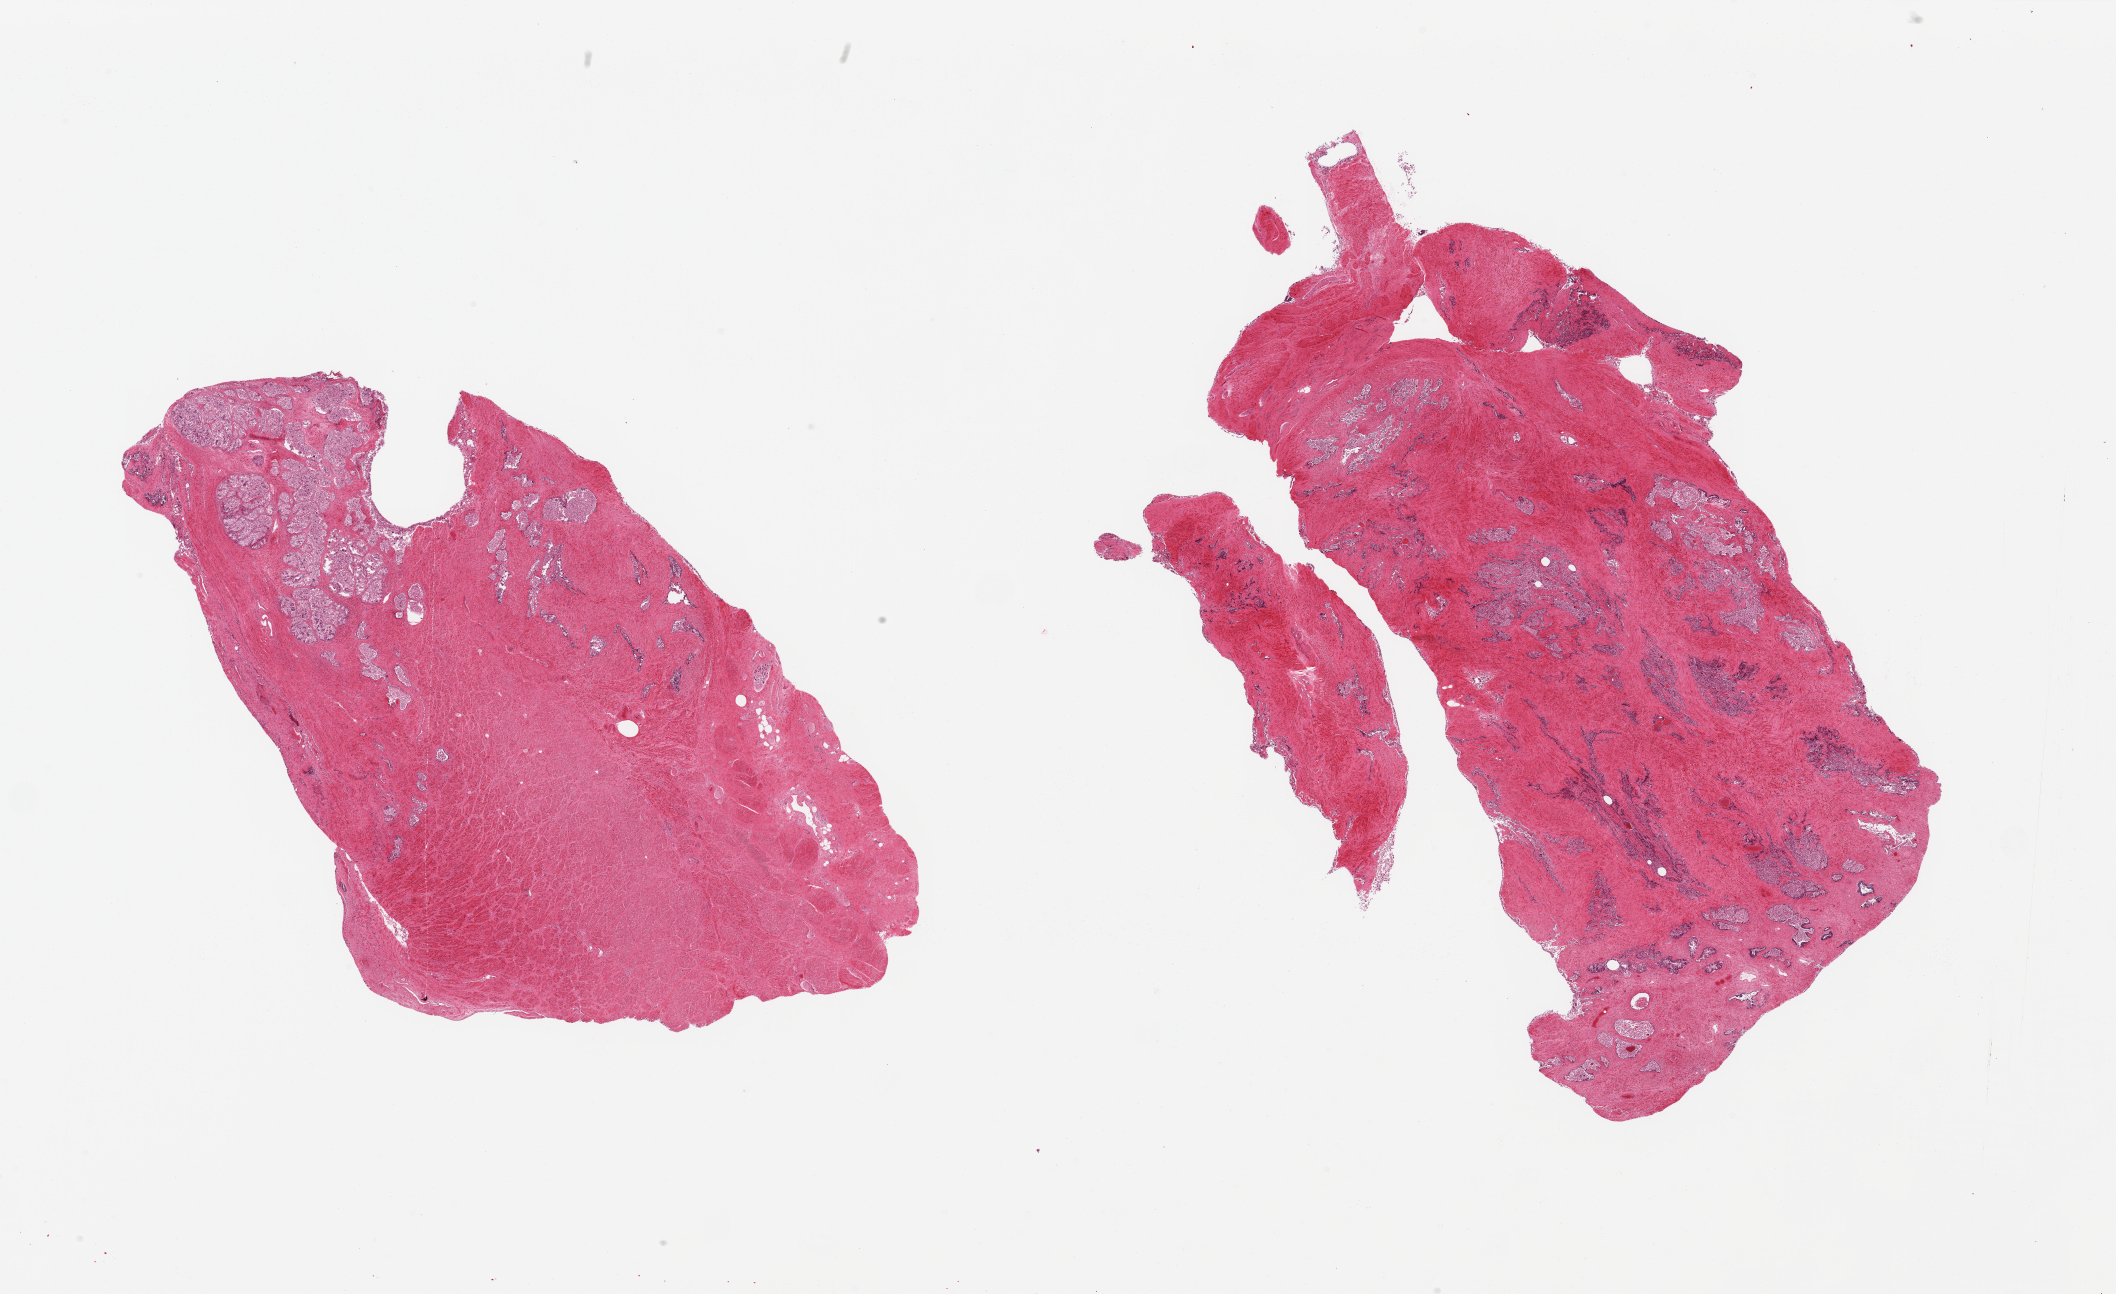
Digitized hematoxylin and eosin (H&E)-stained section, brightfield, a low-resolution overview of the entire scanned area, about 33.5 x 20.5 mm (slide scanned at 20x), PAXgene-fixed paraffin-embedded (PFPE) section, sampled site (target tissue): prostate, tissue donor sample. Donor: male.
Reviewer comment on this tissue sample: 2 pieces;glandular hyperplasia and fibromuscular stroma; glandular epithelium largely sloughed; congestion.